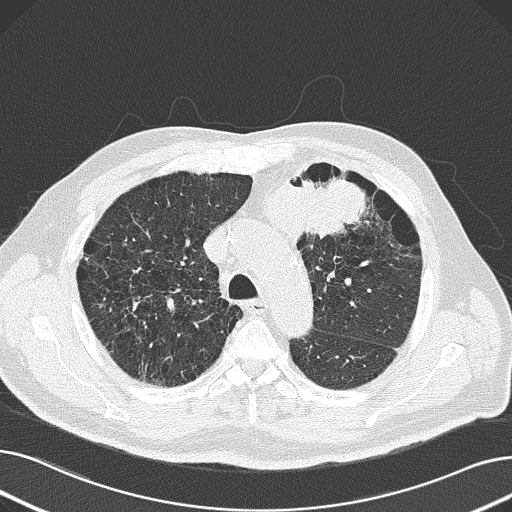
Low-dose screening chest CT, axial slice; first (baseline) screen; lung window (W 1500 / L -600 HU); lung (sharp) reconstruction kernel (B50f); slice 55 of 165 in the series. Male participant, aged 69 years at enrolment.
Expert reader's lesion annotation, bounding box (x1, y1, x2, y2) in pixels: (226, 148, 379, 254). Reader record for this screening exam (exam-level; its link to the box is not recorded): non-calcified nodule or mass ≥4 mm, left upper lobe, 6 × 10 mm, spiculated (stellate) margins, soft tissue attenuation. Official screen result: positive, change unspecified: nodule(s) >= 4 mm or enlarging nodule(s), mass(es), or other non-specific abnormalities suspicious for lung cancer. Participant outcome: lung cancer diagnosed 20 days after this screen — non-small cell carcinoma, left upper lobe, poorly differentiated (G3), stage IB (AJCC 6th edition), 100 mm at pathology.